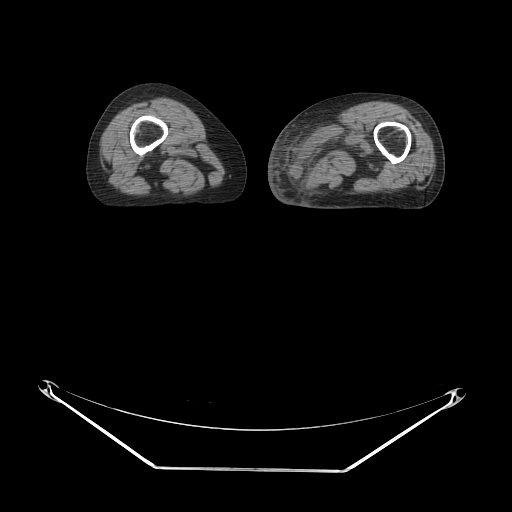
CT of an extremity soft-tissue mass (from a PET/CT study), one axial slice; position 11 of 91 along the scan axis; soft-tissue window (W 400 / L 40 HU); 3.75 mm slice thickness; 512 × 512 image matrix, field of view 500 × 500 mm. Female patient. Case-level facts recorded for this patient, not image findings: histological type: pleomorphic leiomyosarcoma; grade: high; site of the primary tumour: left thigh.
Annotated regions visible in this slice (expert contour drawn on MRI and transferred to this co-registered scan by the dataset authors):
- gross tumour volume including surrounding oedema: bounding box <297,114,380,186> (left, top, right, bottom; pixels)